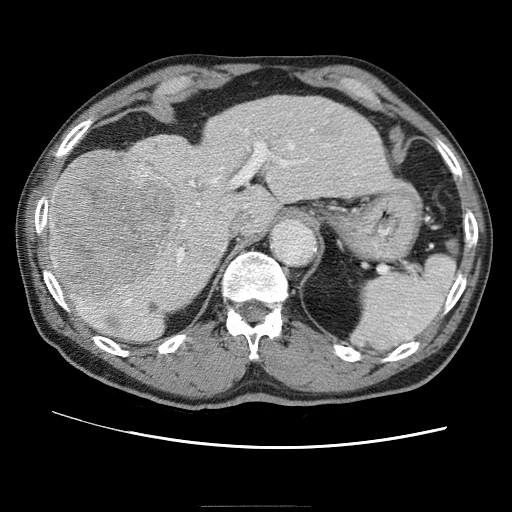
Contrast-enhanced abdominal CT (liver protocol), one axial slice. Slice 40 of 75 in the series (ordered by position). Reconstruction kernel STANDARD. 120 kVp. One of 2 acquisitions stored at this slice position. Soft-tissue window (W 400 / L 40 HU). 2.5 mm slice thickness. 512 × 512 image matrix, field of view 360 × 360 mm. Case-level facts recorded for this patient, not image findings: diagnosis: hepatocellular carcinoma (patient treated with transarterial chemoembolisation; whether this scan precedes or follows treatment is not stated here); TNM stage (as recorded): Stage-II; Child-Pugh class: A; tumour nodularity: multinodular; tumour size: 2 cm.
Annotated regions visible in this slice (semi-automatic segmentation, software-assisted and operator-edited):
- liver parenchyma outside the tumour (the mass and vessels are separate outlines, so this box may not span the whole liver): bounding box [x1, y1, x2, y2] px = [46, 96, 396, 342]
- mass: [49, 153, 178, 294]
- liver vessels: [82, 133, 312, 315]